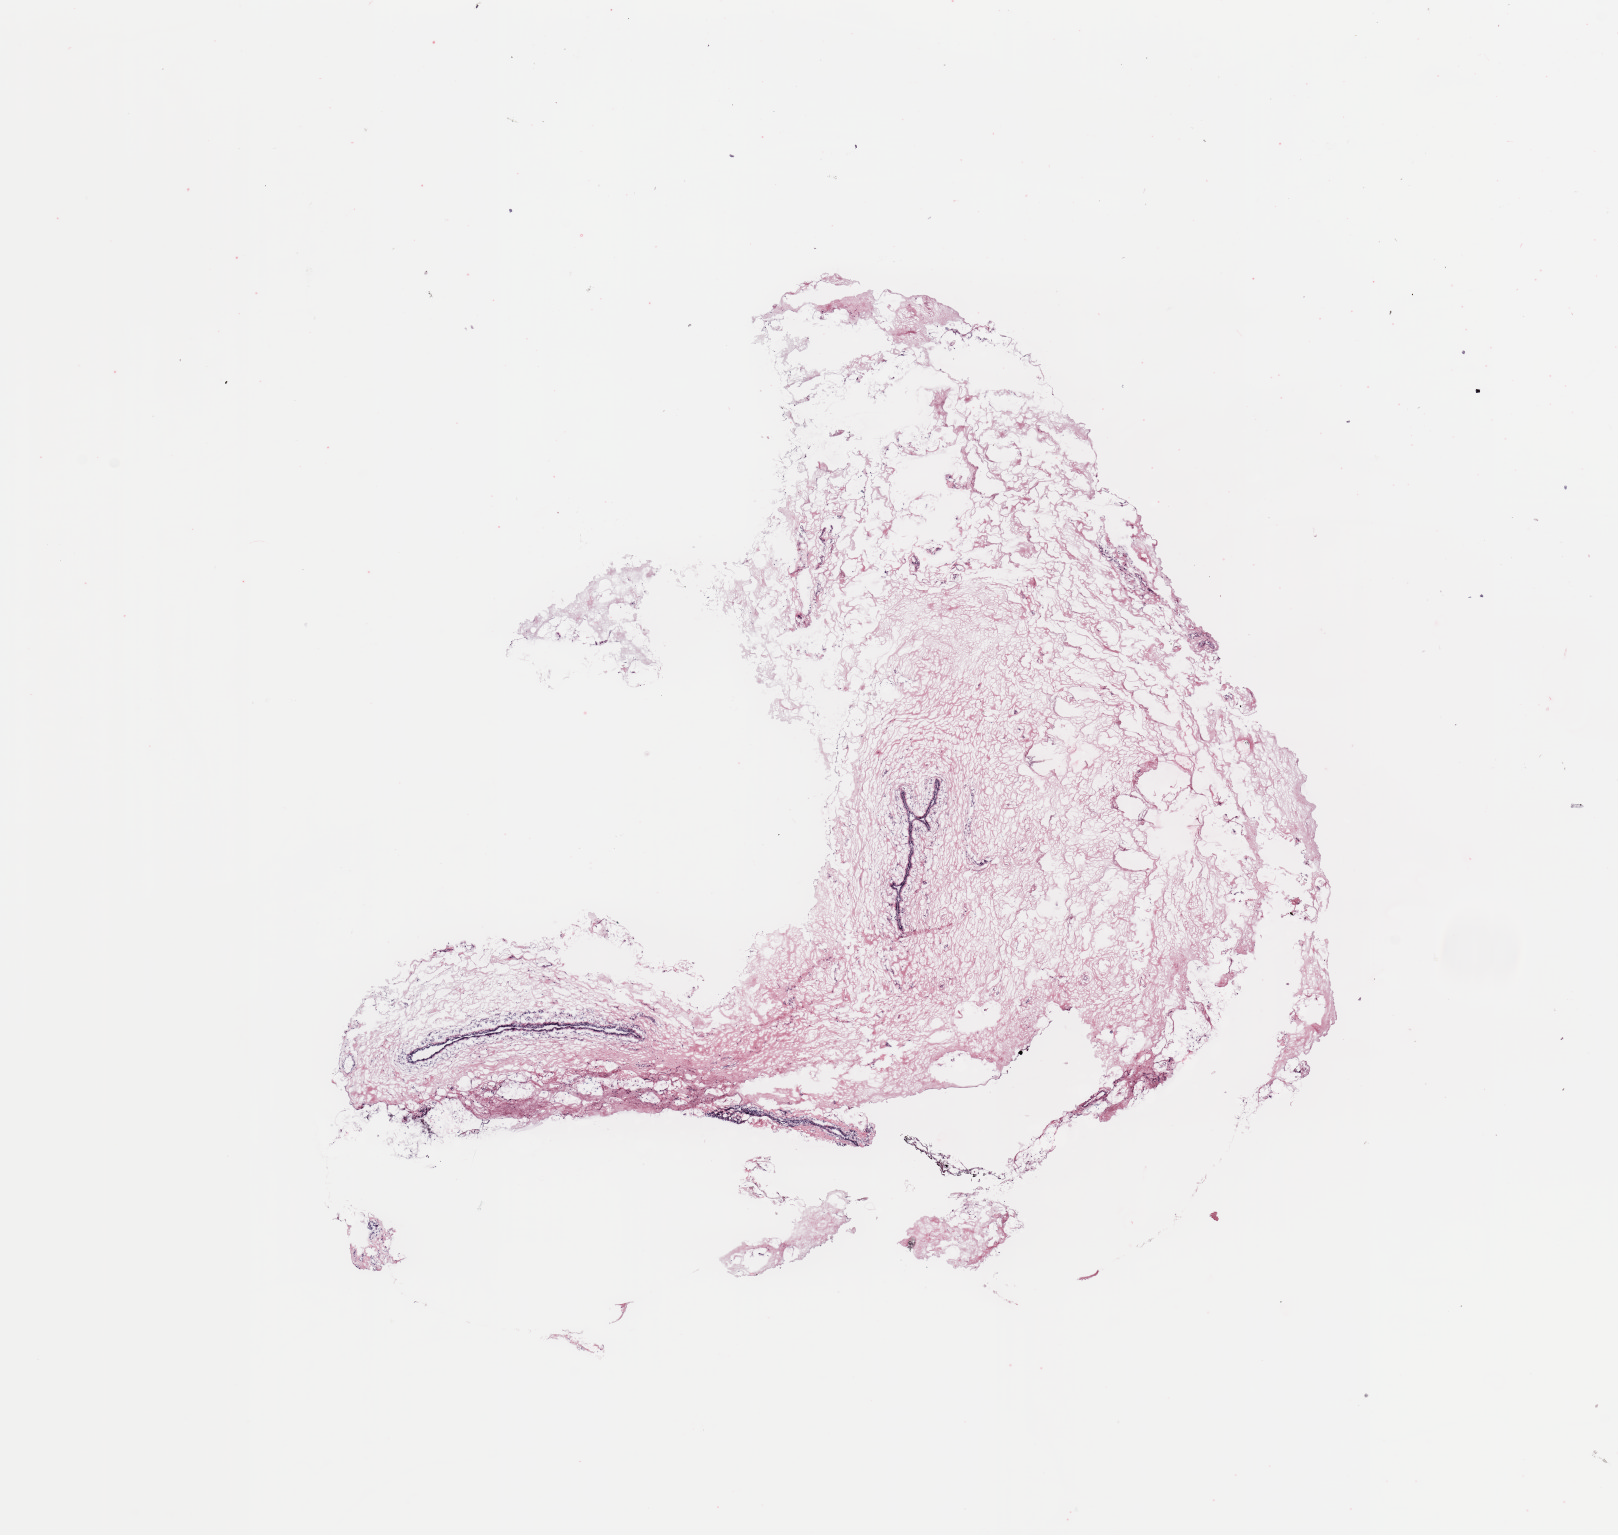
H&E-stained whole-slide image, whole scanned area (about 12.8 x 12.1 mm, acquisition: 20x scan) shown as a low-resolution overview; breast, tumour tissue. Female, 61 y/o.
AJCC pathologic stage: IIA. Histologic diagnosis: Infiltrating duct carcinoma, NOS.